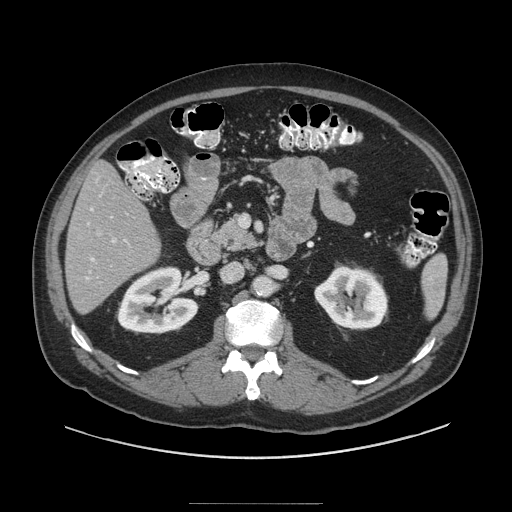
Contrast-enhanced abdominal CT (liver protocol), one axial slice. Position 40 of 91 along the scan axis. 140 kVp. Soft-tissue window (W 400 / L 40 HU). 512 × 512 image matrix, field of view 440 × 440 mm. Case-level facts recorded for this patient, not image findings: diagnosis: hepatocellular carcinoma (patient treated with transarterial chemoembolisation; whether this scan precedes or follows treatment is not stated here); TNM stage (as recorded): Stage-I; Child-Pugh class: A; tumour differentiation: well differentiated.
Annotated regions visible in this slice (semi-automatic segmentation, software-assisted and operator-edited):
- liver parenchyma outside the tumour (the mass and vessels are separate outlines, so this box may not span the whole liver): bounding box [x1, y1, x2, y2] px = [64, 162, 160, 313]
- liver vessels: [85, 180, 128, 280]